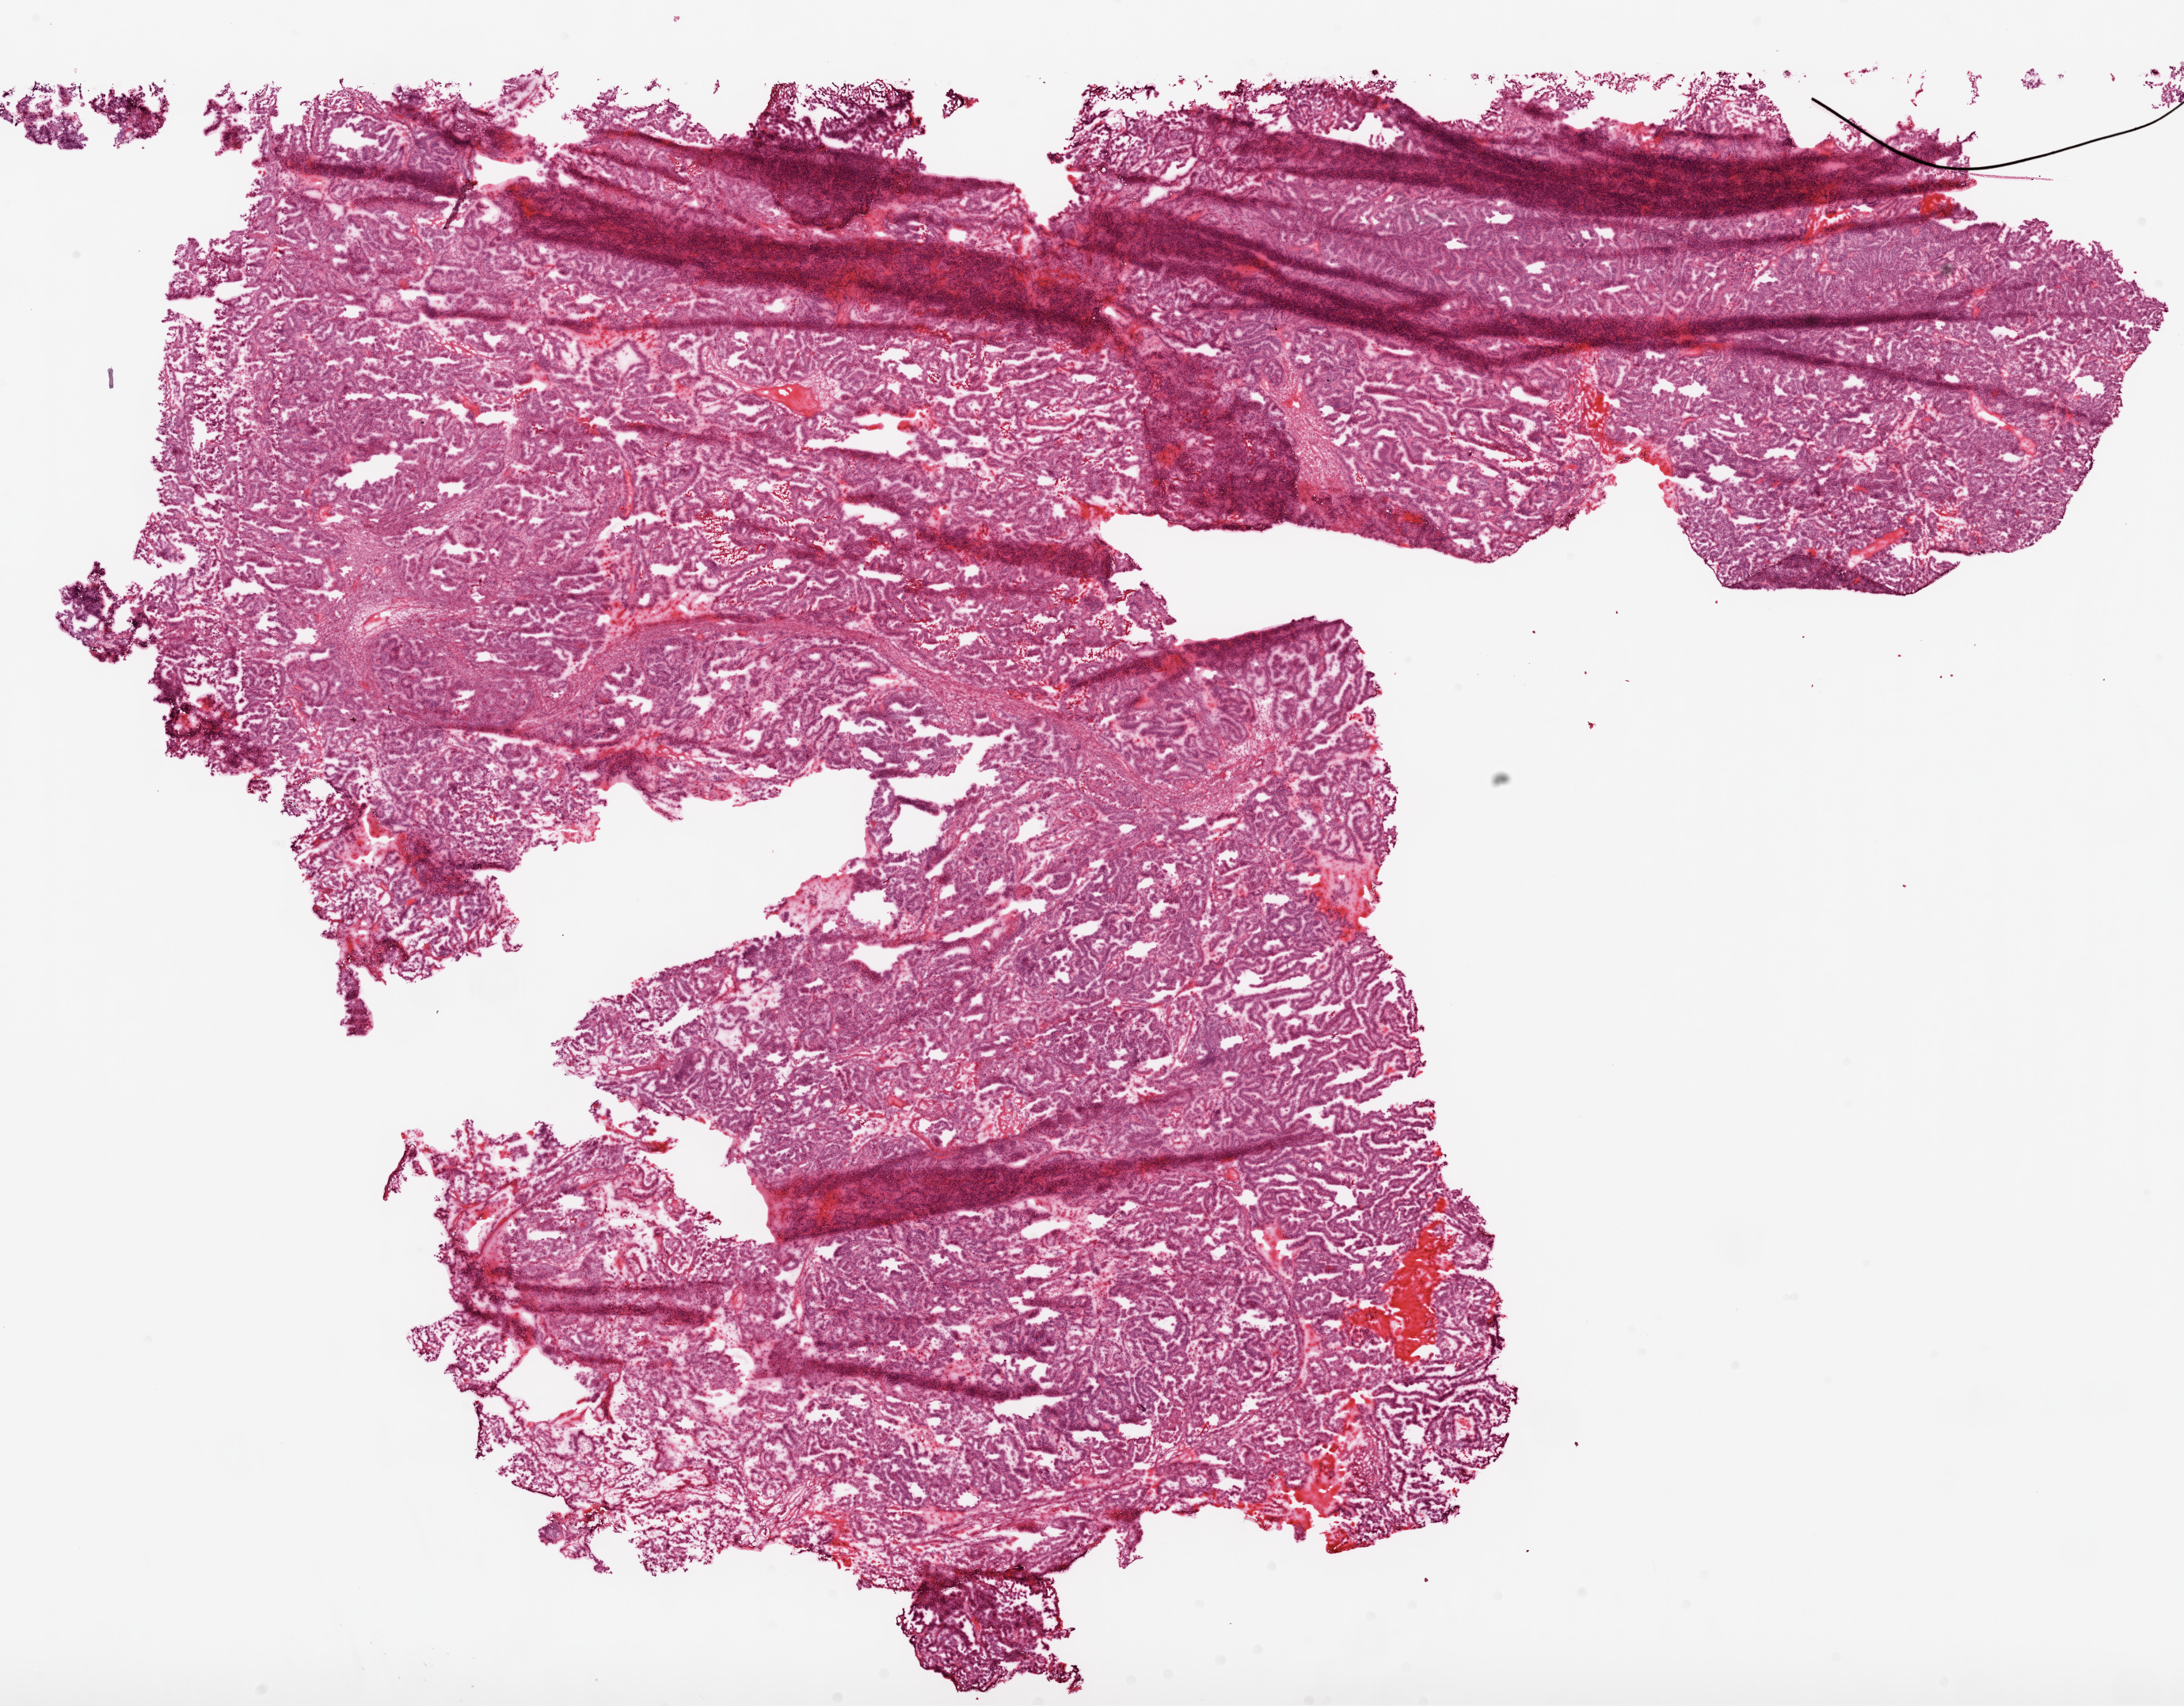
H&E whole-slide image — low-resolution overview of the scanned area, about 22.2 x 17.4 mm, frozen section from the top of the tissue portion, ovary, primary tumour sample. Female patient; age at initial diagnosis 50 years. Histologic grade: G3 (poorly differentiated). Composition of this section per pathologist review: tumour cells 95%, tumour nuclei 95%, normal cells 0%, stromal cells 5%, necrosis 0%.
Laterality: bilateral. Diagnosis: Serous cystadenocarcinoma, NOS. FIGO stage: IIIC.